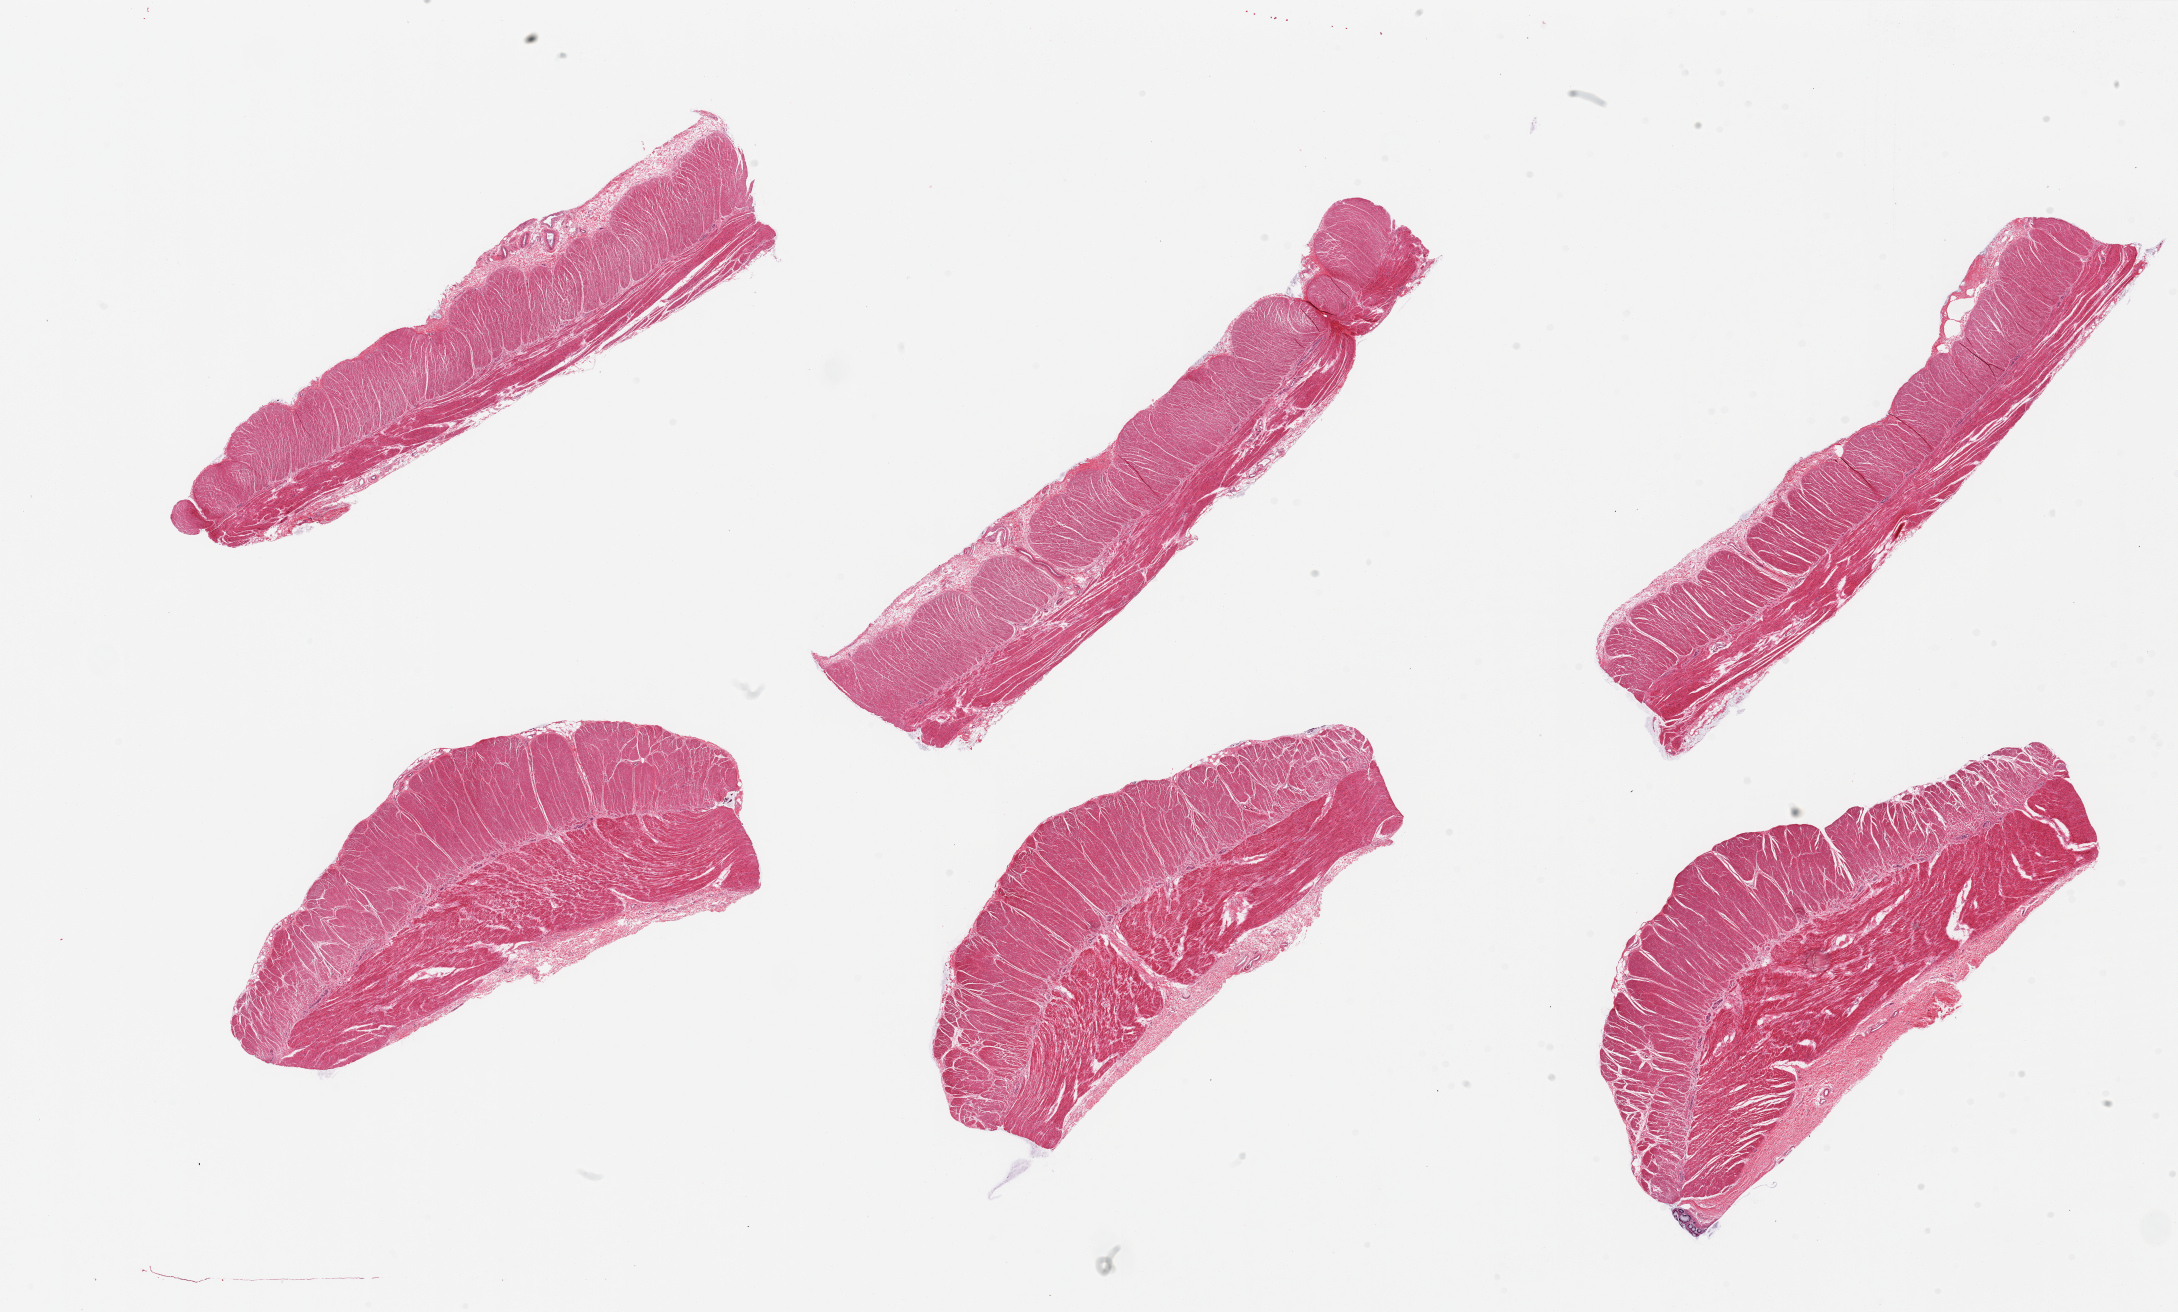
Digitized haematoxylin and eosin-stained section, brightfield, shown as a low-resolution overview of the whole scanned area (about 34.5 x 20.8 mm, acquisition: 20x scan); PAXgene-fixed paraffin-embedded (PFPE) section; section of sigmoid colon (target tissue); donor tissue sample. Donor: female.
Reviewer comment on this tissue sample: 6 pieces, all muscularis.